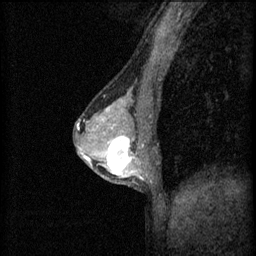
Breast MRI (dynamic contrast-enhanced), one sagittal slice. Position 31 of 60 along the scan axis. 3 images stored at this slice position (order not interpretable as contrast timing). 1.5 T. TE 4.2 ms, TR 8.2 ms. 256 × 256 image matrix. Patient: female, 44 years.
Annotated regions visible in this slice (semi-automatic segmentation, software-assisted and operator-edited):
- analysis volume of interest (the breast-tissue region the enhancement analysis was run in; not a lesion): bounding box (x1, y1, x2, y2) in pixels: (102, 132, 151, 181)
- tumour enhancement mask (voxels above the 70 % enhancement threshold inside the analysis volume of interest): (104, 136, 143, 177)